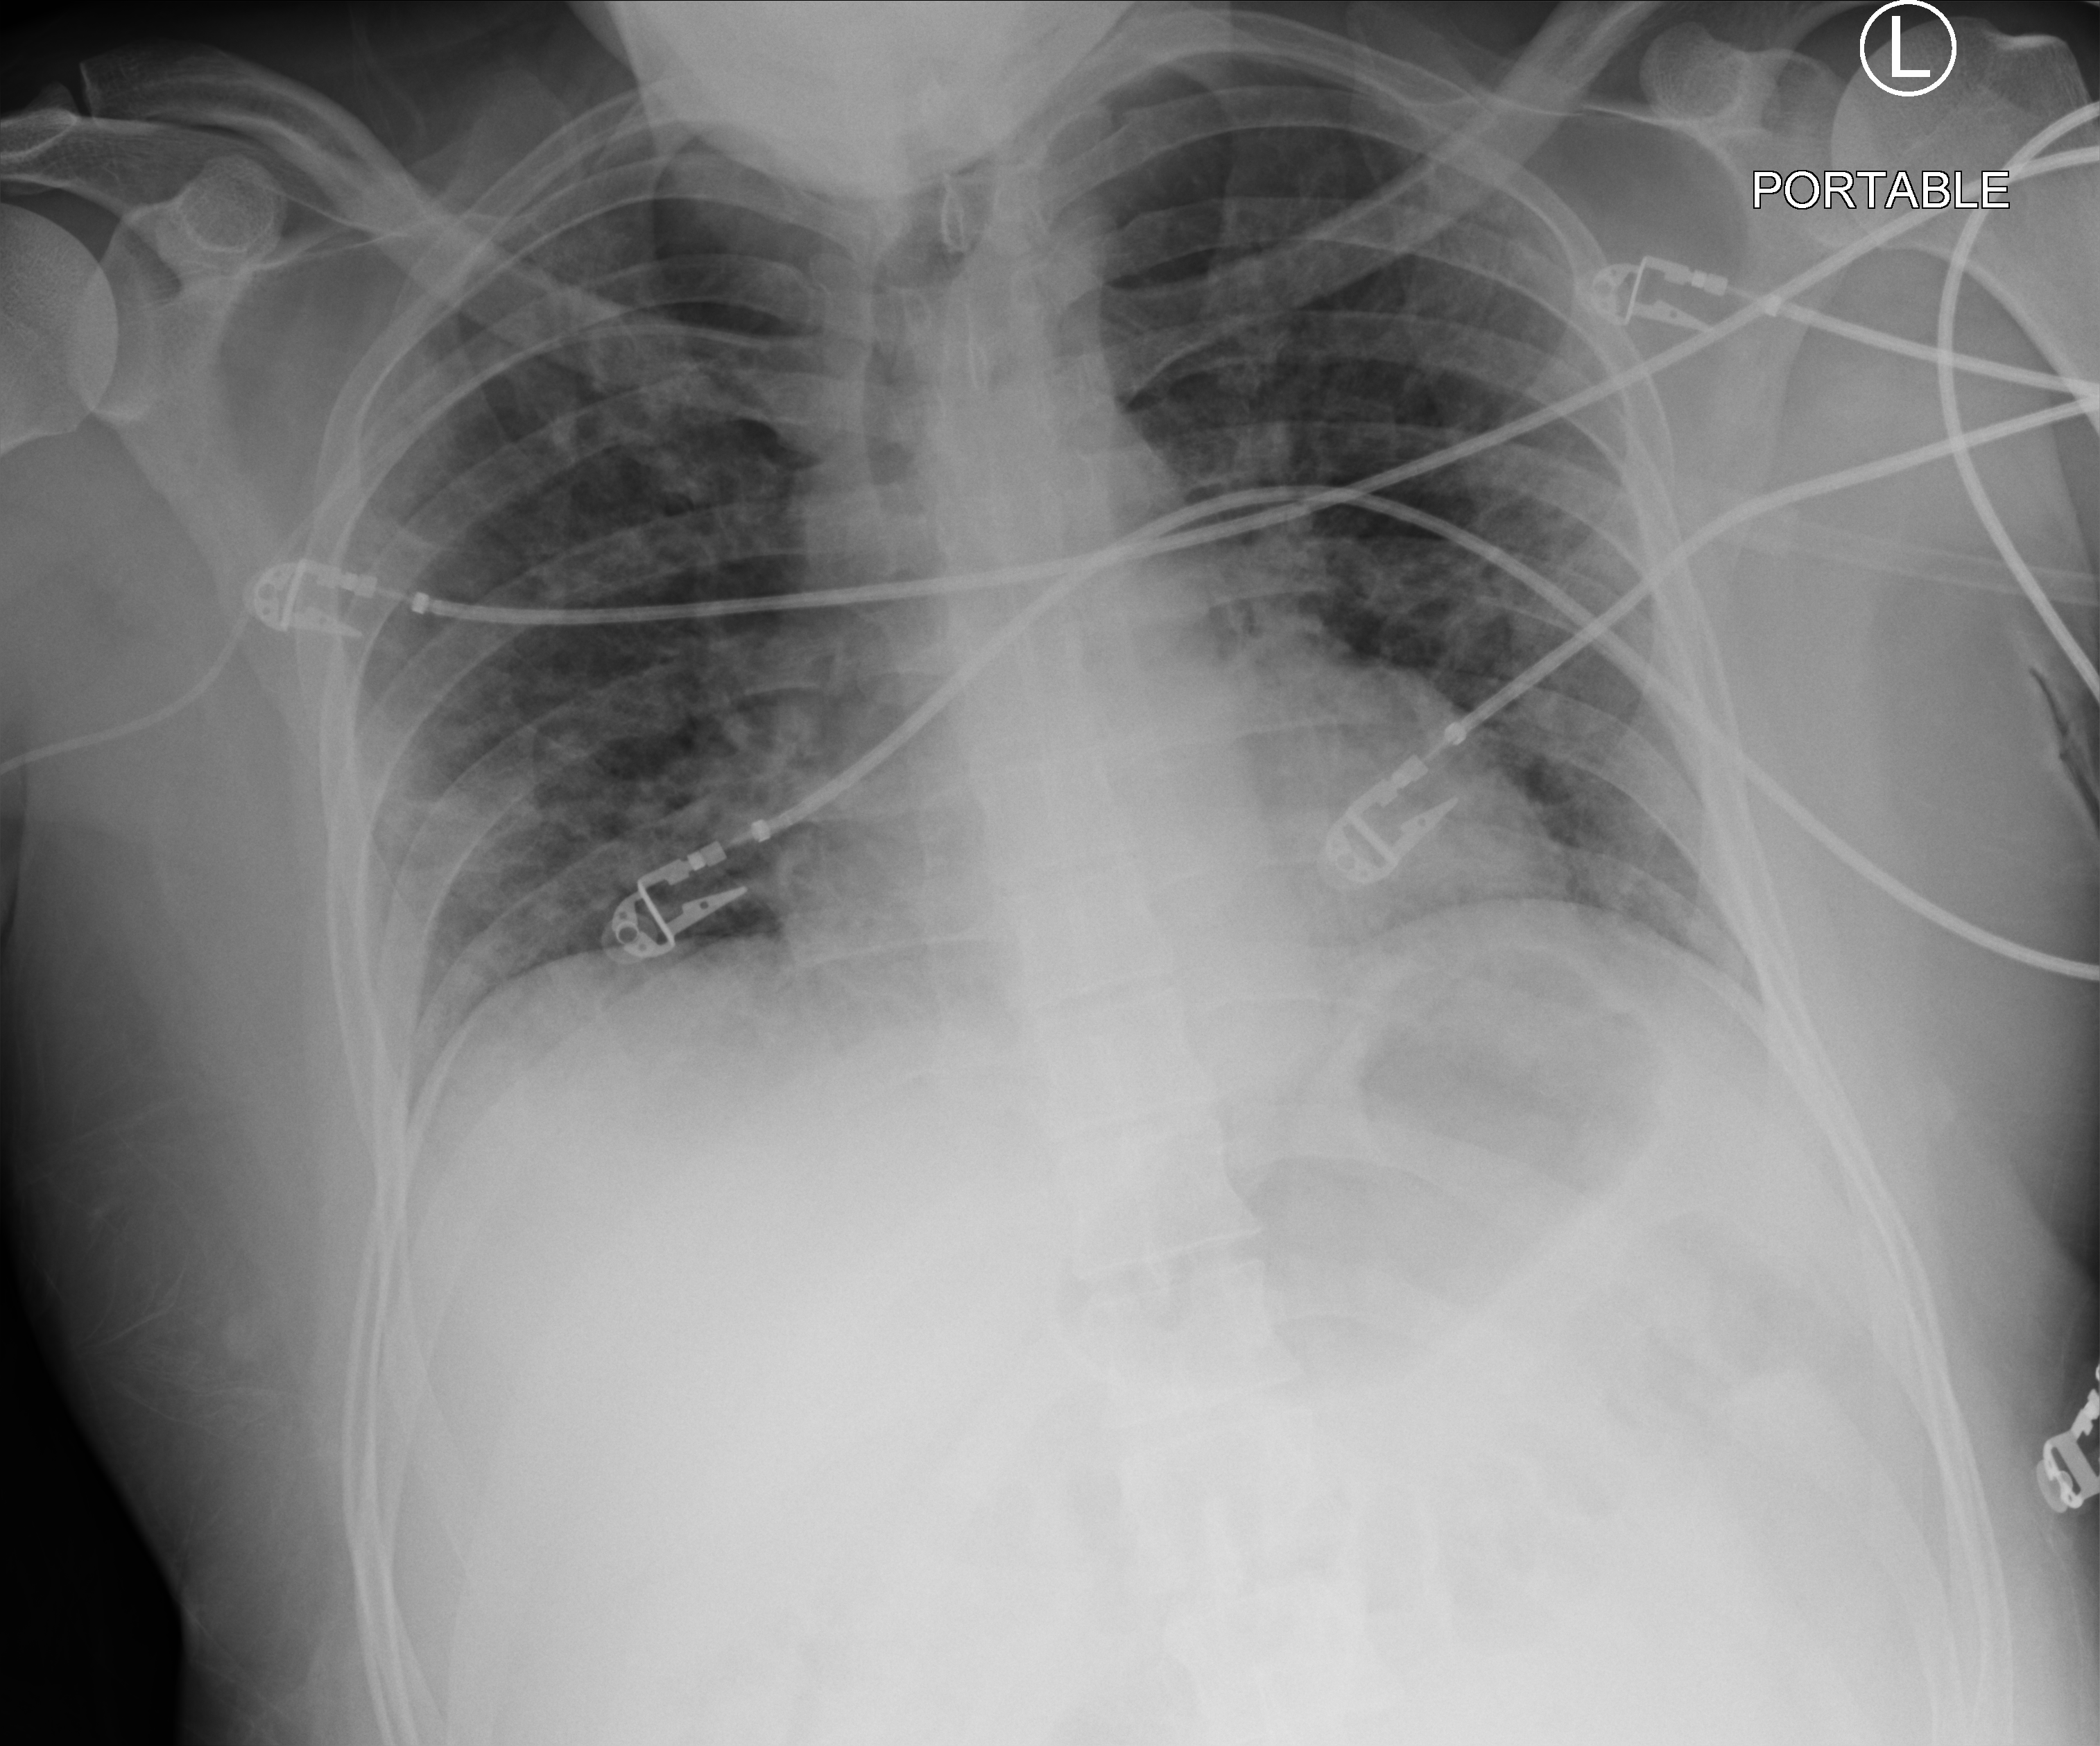
Portable chest radiograph. Patient hospitalised with COVID-19; male, aged 18–59 years.
Hospital-stay facts (about this admission, not read from this image; timing relative to this image not recorded):
- mechanically ventilated during this hospital stay: yes
- admitted to intensive care during this hospital stay: yes